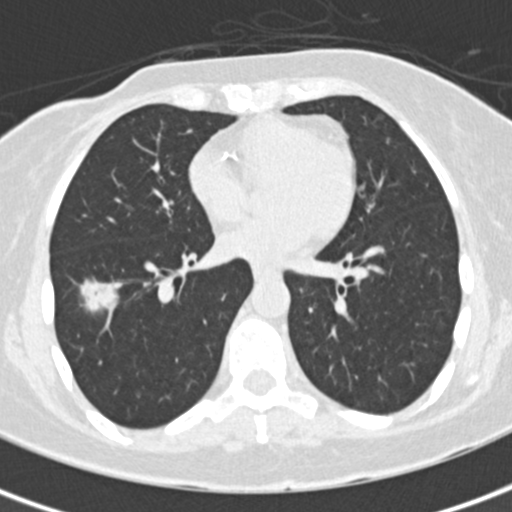
Low-dose screening chest CT, one axial slice. Position 77 of 171 along the scan axis. Reconstruction kernel B30f. Lung window (W 1500 / L -600 HU). 2 mm slice thickness. 512 × 512 image matrix, field of view 284 × 284 mm.
Outlined on this slice (manually delineated by an expert):
- lesion 1 (tumor, lower lobe of right lung): bounding box [x1, y1, x2, y2] px = [78, 279, 115, 313]